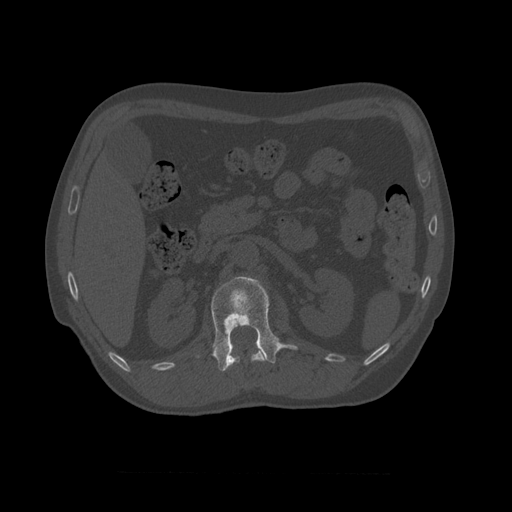
CT including the spine, one axial slice. Slice 359 of 450 in the series (ordered by position). 120 kVp. Bone window (W 1800 / L 400 HU). 1.25 mm slice thickness. 512 × 512 image matrix, field of view 405 × 405 mm. Patient age 75 years. Case-level facts recorded for this patient, not image findings: primary cancer: prostate.
Outlined on this slice (semi-automatically segmented with operator editing):
- L1 vertebra: box from (x=196, y=277) to (x=299, y=372) px
- T10 vertebra: (x=220, y=340)–(x=265, y=371)
- T11 vertebra: (x=225, y=352)–(x=267, y=371)